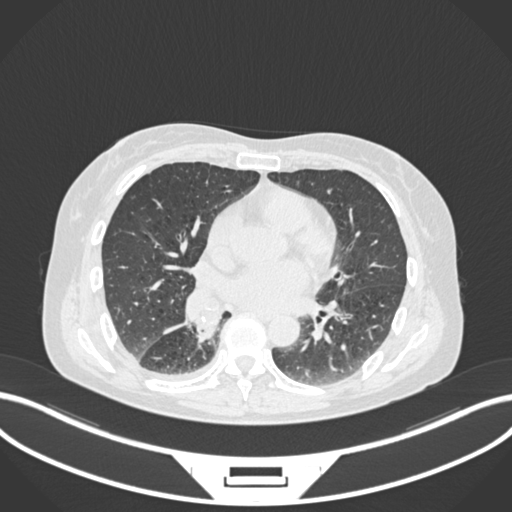
Chest CT, one axial slice. Reconstruction kernel B30f. 120 kVp. Lung window (W 1500 / L -600 HU). 1 mm slice thickness. 512 × 512 image matrix. Patient: female, 63 years. From the clinical record (not read from this slice): clinical TNM (as recorded): T1c N0 M0.
Outlined on this slice (rectangle marked by the reading radiologist):
- lung tumour (recorded histology: adenocarcinoma): bounding box (x1, y1, x2, y2) in pixels: (191, 299, 231, 346)